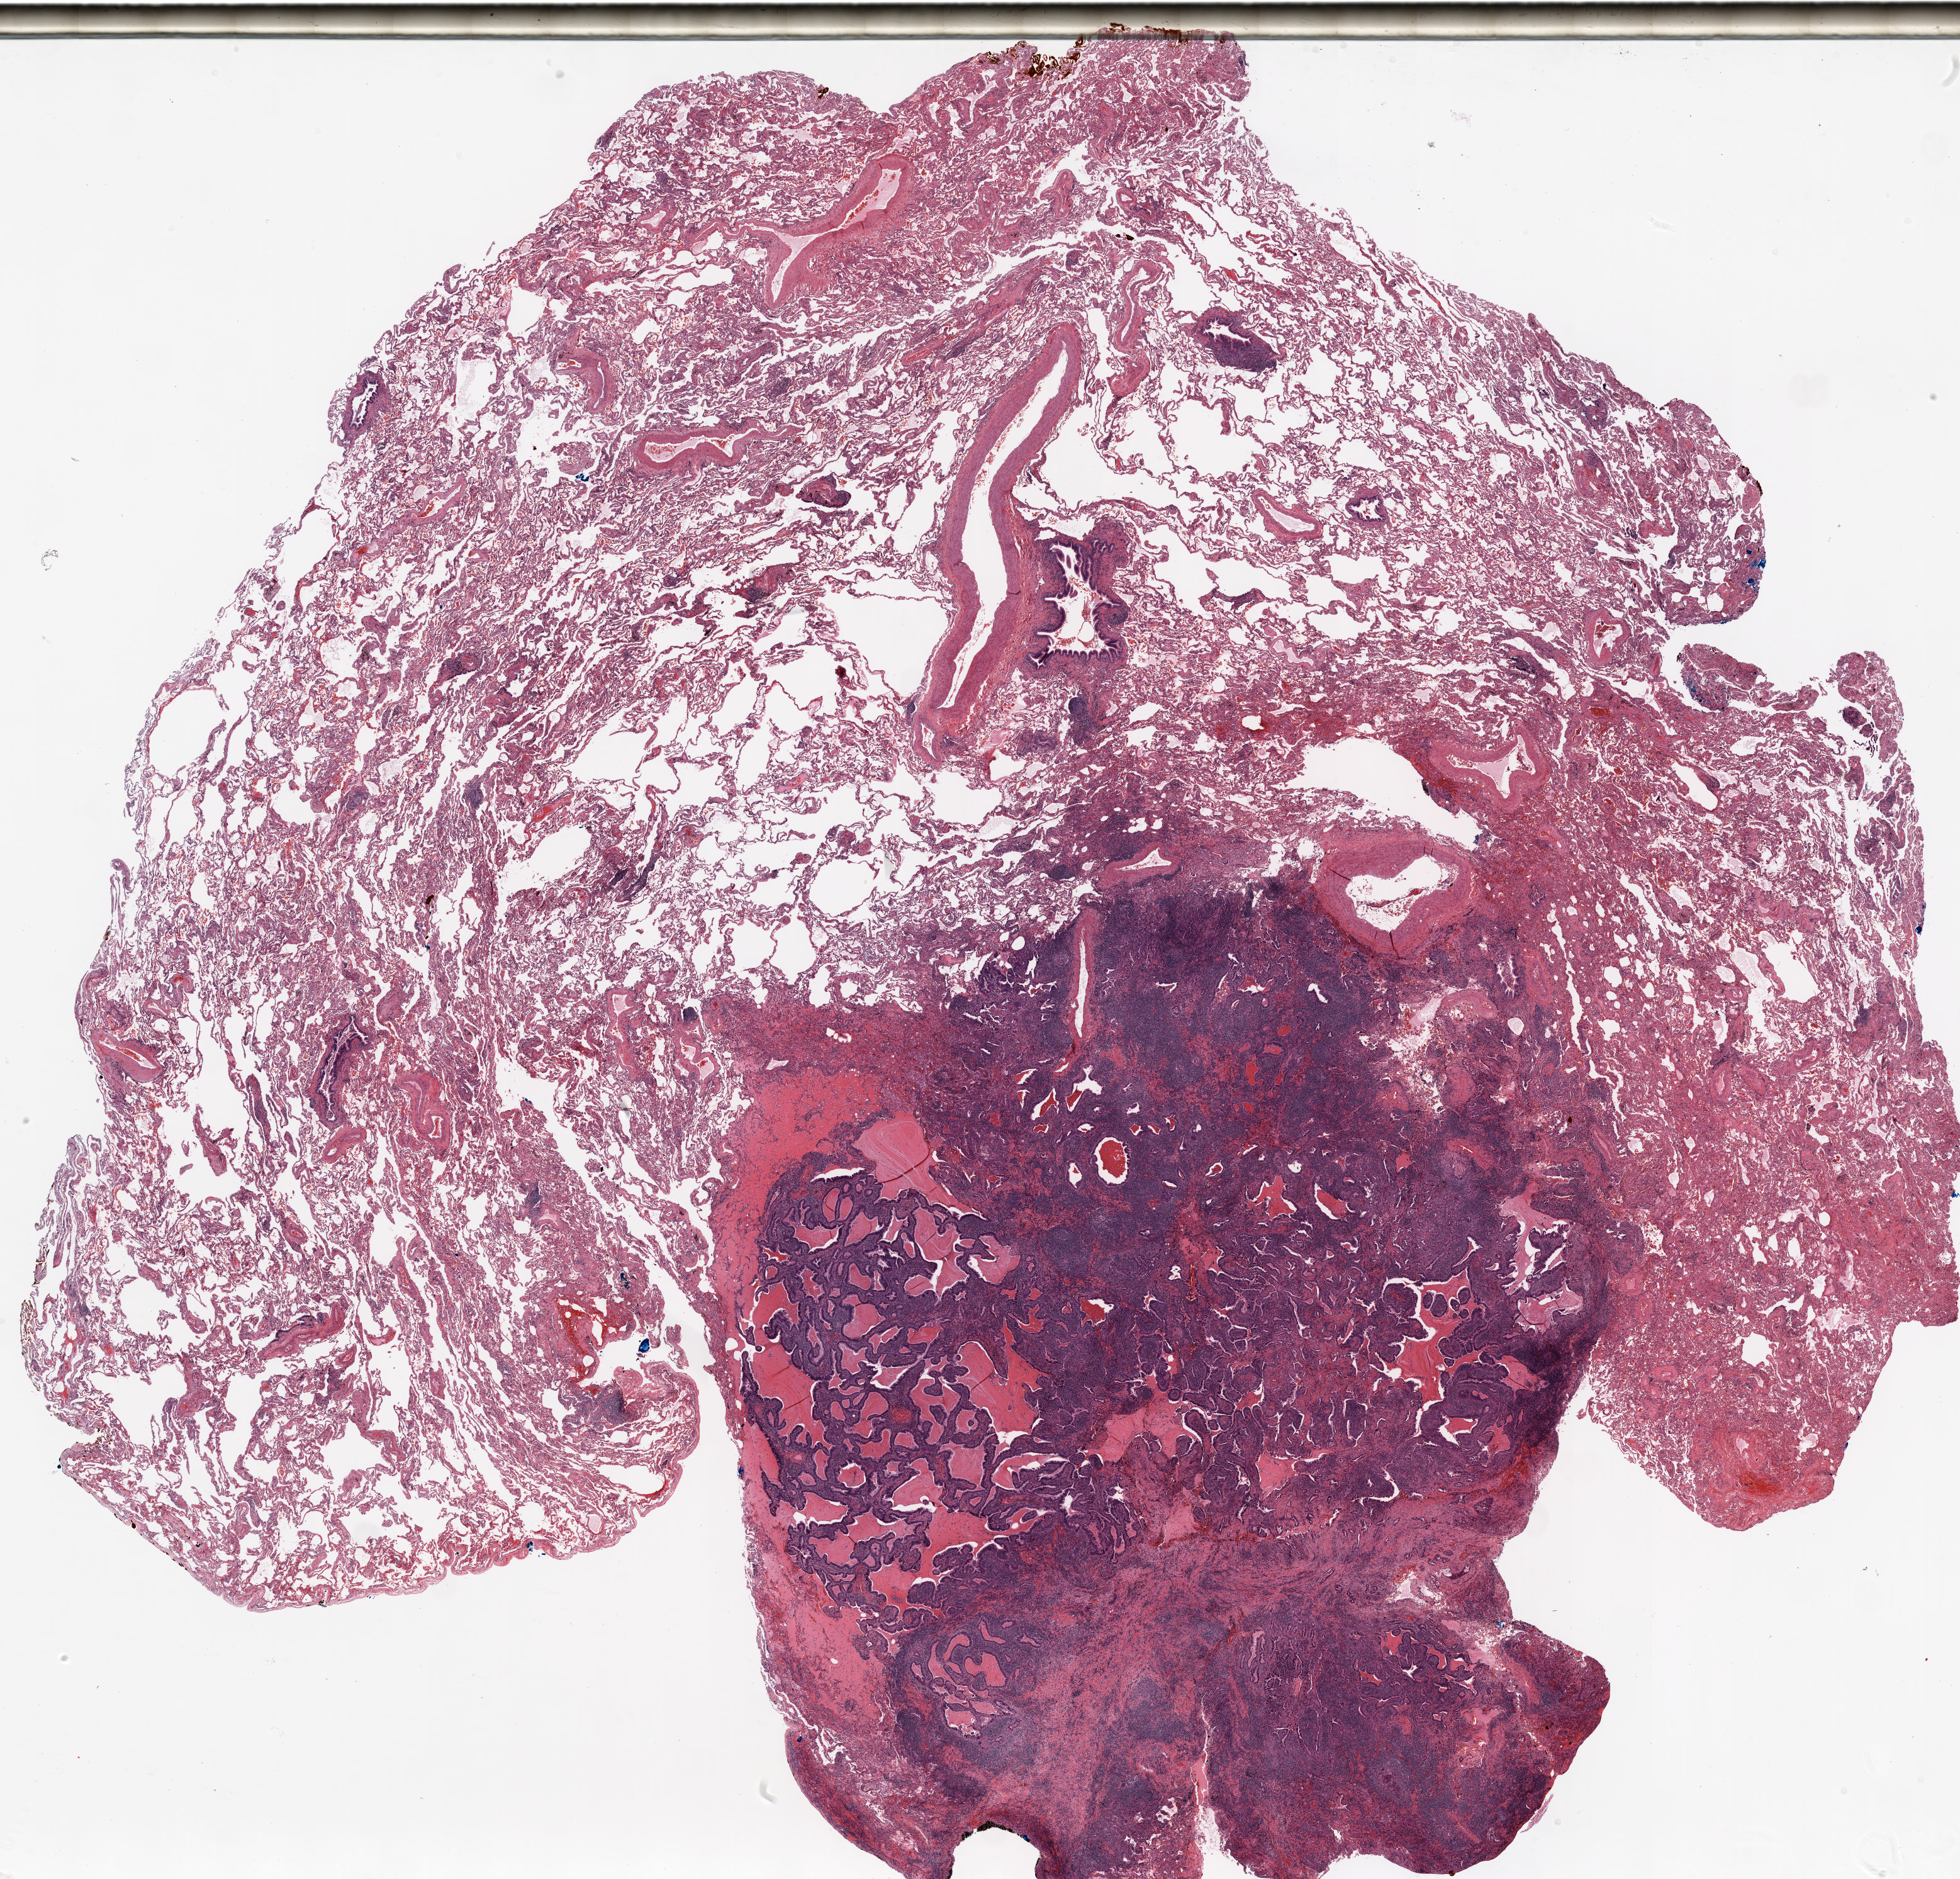
Hematoxylin and eosin (H&E) stained whole-slide image — shown as a low-resolution overview of the whole scanned area (about 25.0 x 24.0 mm, from a 20x scan); formalin-fixed paraffin-embedded (FFPE) section; lung tissue. Female patient, aged 72 at enrolment. Former smoker at enrolment. Grade: moderately differentiated (G2).
Participant's lung-cancer diagnosis: Adenocarcinoma, NOS (ICD-O-3 8140/3). Stage (AJCC 6th edition): IA. Primary tumour location (clinical record): left upper lobe. Tumour size (pathology): 25 mm. Note: participant had 2 primary lung cancers recorded; fields above describe the first.